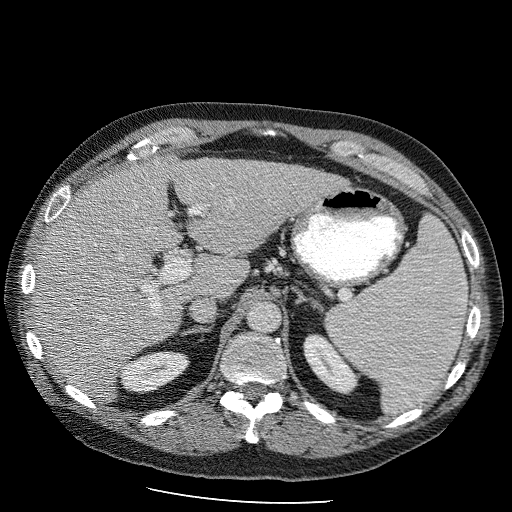
Contrast-enhanced abdominal CT (liver protocol), one axial slice. Slice 63 of 98 in the series (ordered by position). Reconstruction kernel STANDARD. 120 kVp. Soft-tissue window (W 400 / L 40 HU). 2.5 mm slice thickness. 512 × 512 image matrix. From the clinical record (not read from this slice): diagnosis: hepatocellular carcinoma (patient treated with transarterial chemoembolisation; whether this scan precedes or follows treatment is not stated here); TNM stage (as recorded): Stage-II; Child-Pugh class: B; tumour nodularity: uninodular.
Structures marked on this image (semi-automatically segmented with operator editing):
- liver parenchyma outside the tumour (the mass and vessels are separate outlines, so this box may not span the whole liver): bounding box [x1, y1, x2, y2] px = [32, 154, 348, 404]
- liver vessels: [124, 194, 338, 332]